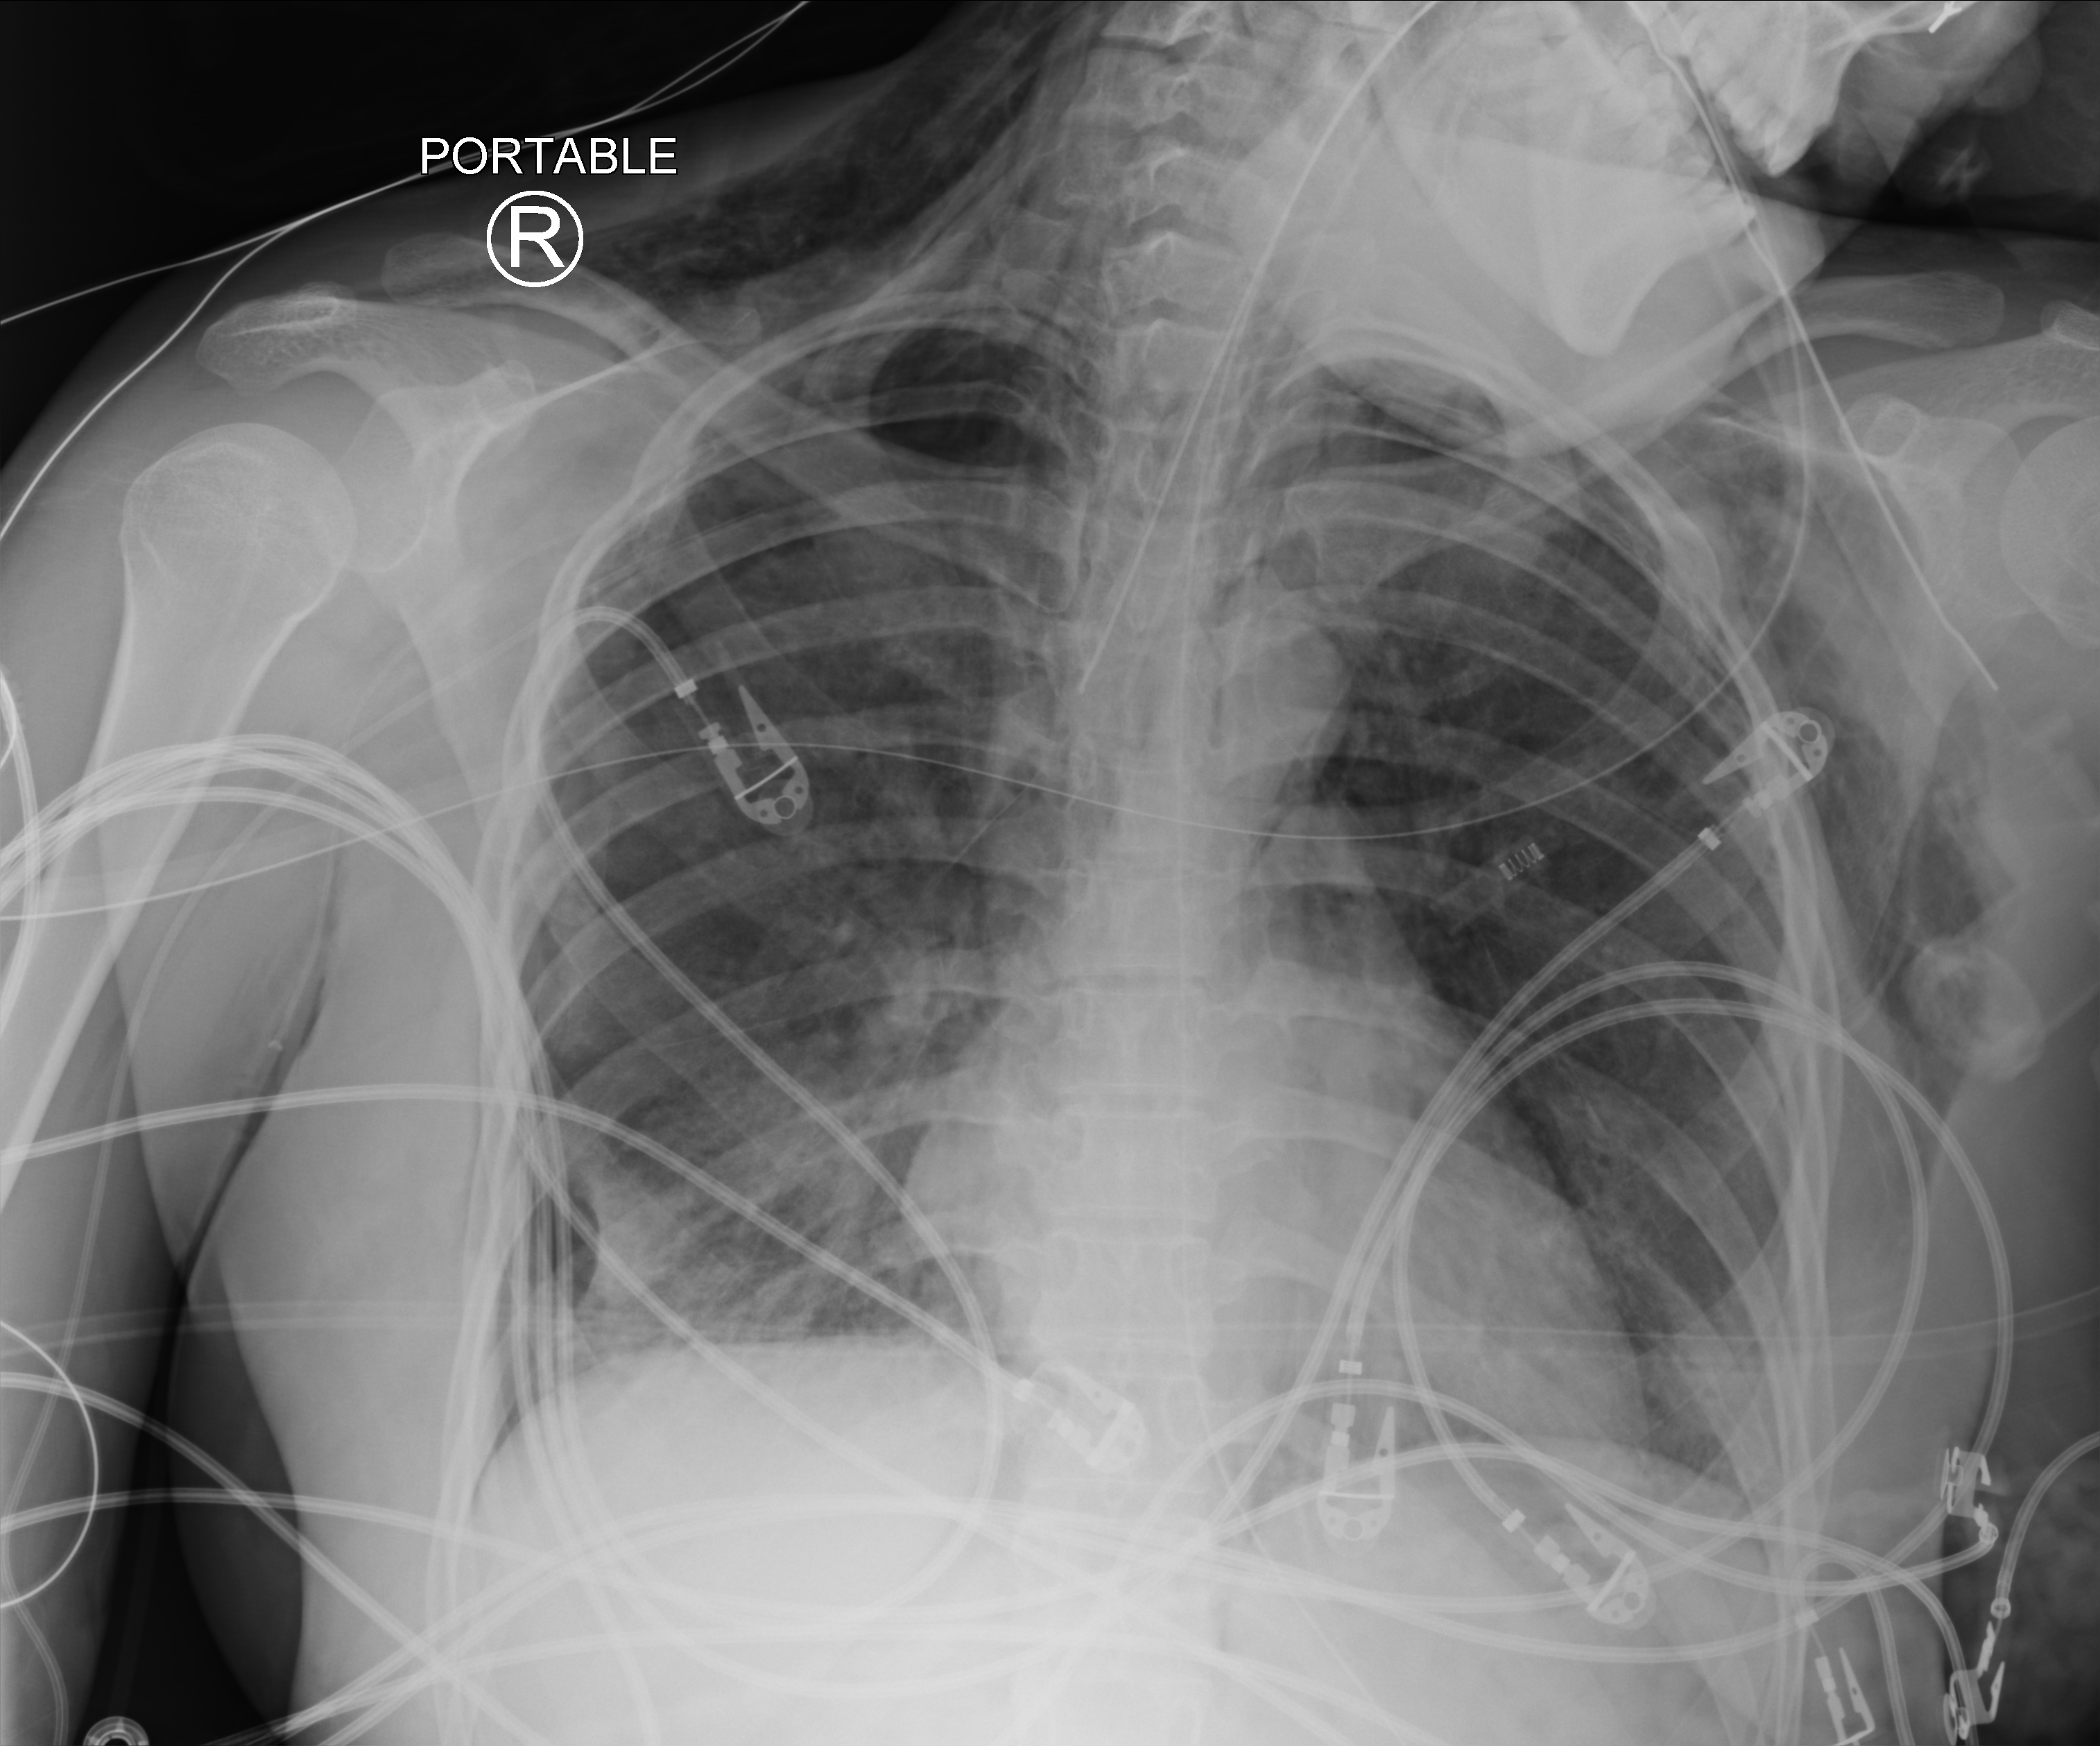
Chest X-ray (portable), anteroposterior (AP) projection. Patient hospitalised with COVID-19, aged 18–59 years.
From the hospital-stay record, not from the radiograph (when in the stay this image was taken is not recorded): diabetes (admission record): no; length of hospital stay: 30 days; hypertension (admission record): no.